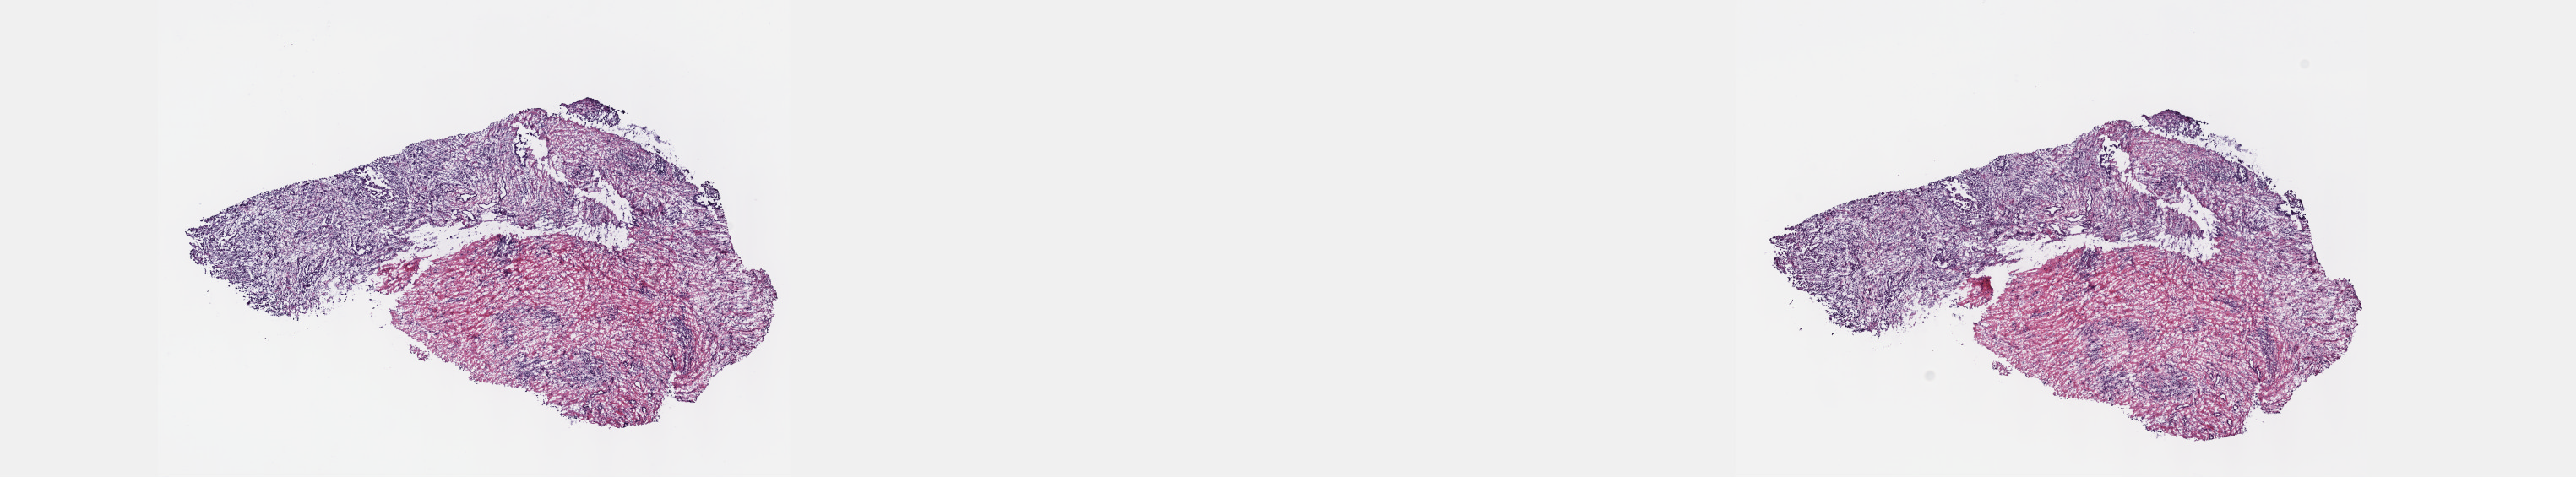
Whole-slide histology image, H&E, whole scanned area (about 24.6 x 4.6 mm, slide scanned at 40x) shown as a low-resolution overview, frozen section, sample: primary tumour, esophagus. Male, age 80 years at initial diagnosis. Histologic grade: G2 (moderately differentiated). Pathologist review of this section (percent, as recorded): tumour cells 100%, tumour nuclei 60%, normal cells 0%, stromal cells 0%, necrosis 0%. Infiltration values recorded for this section: lymphocyte infiltration 8%, monocyte infiltration 0%, neutrophil infiltration 0%.
TNM: T3 N0 M0. Diagnosis: Adenocarcinoma, NOS (lower third of esophagus). Lymph nodes positive (case pathology): 0 of 3 examined. AJCC pathologic stage: IIA (5th edition).